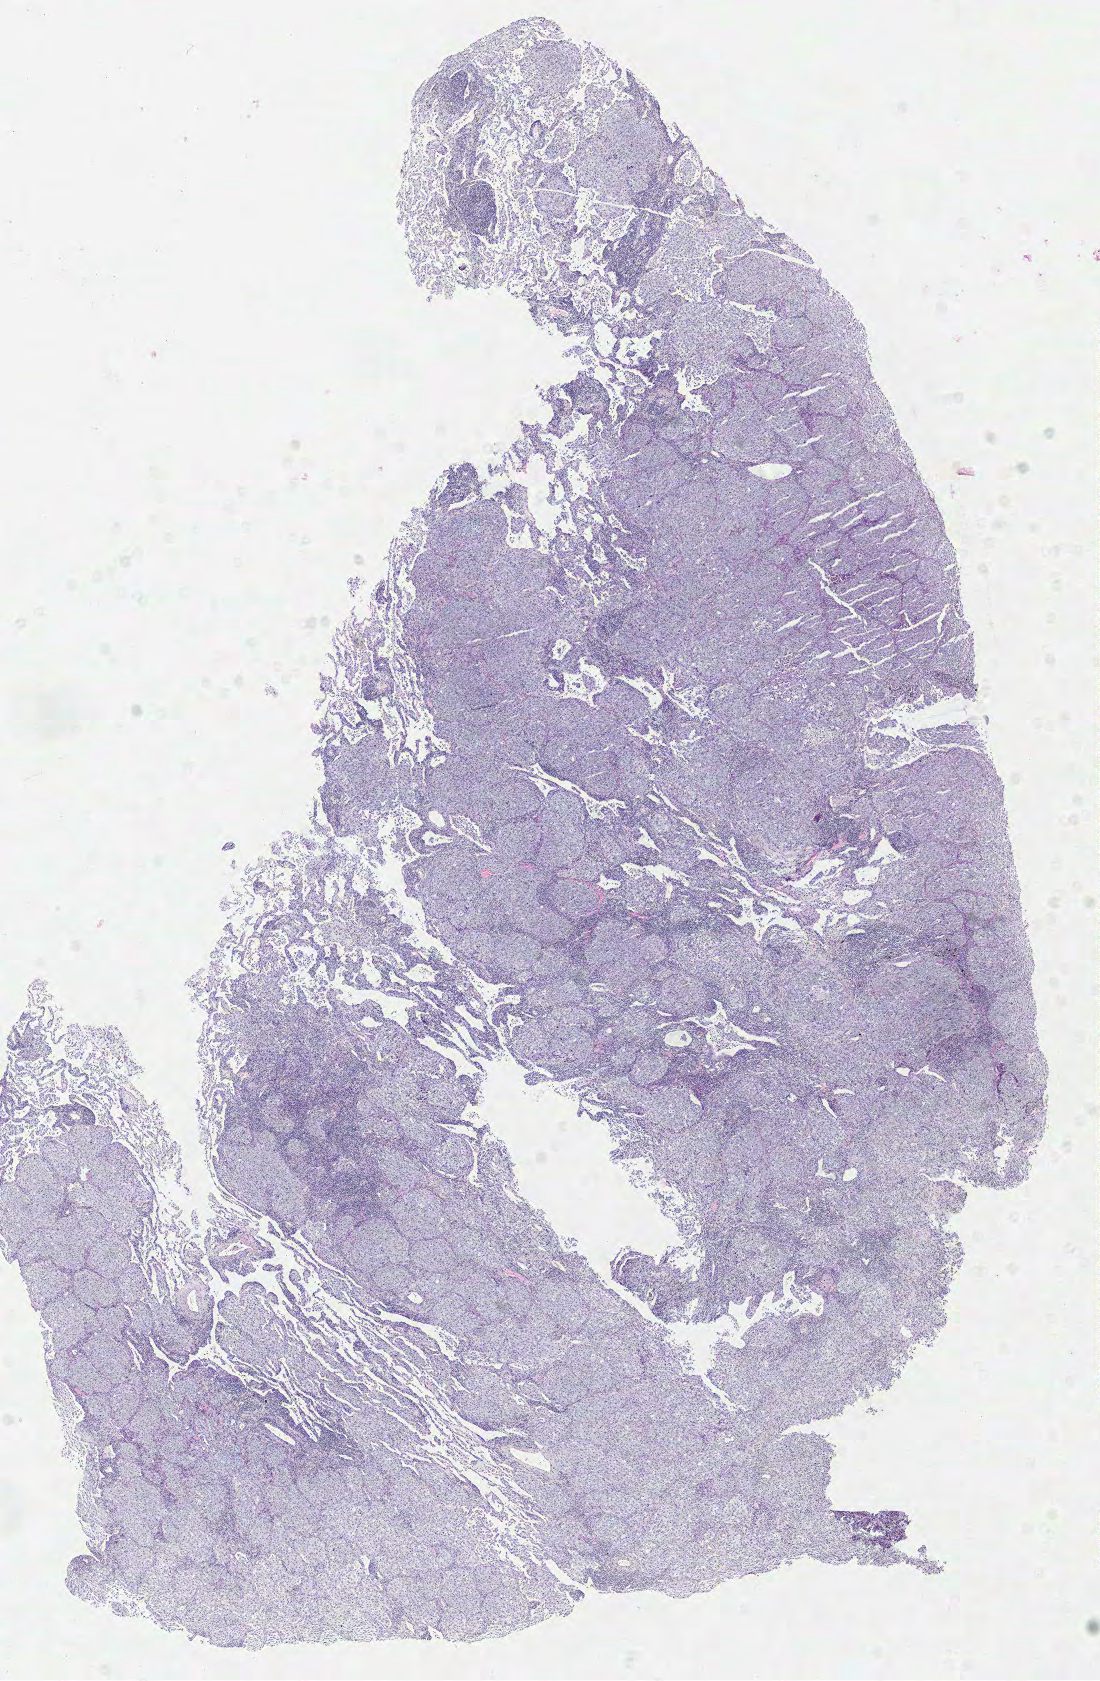
H&E whole-slide image — shown as a low-resolution overview of the whole scanned area (about 8.7 x 13.3 mm, slide scanned at 40x). Formalin-fixed paraffin-embedded (FFPE) diagnostic section. Primary tumour sample from the lung. Patient: male, age at initial diagnosis 66 years.
• diagnosis: Squamous cell carcinoma, NOS (lower lobe, lung)
• AJCC pathologic stage: IIIB (6th edition)
• laterality: right